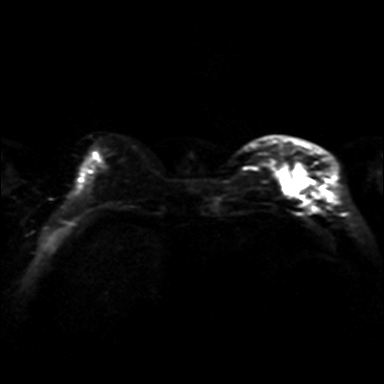
Breast MRI, one axial slice. Slice 9 of 36 in the series (ordered by position). Diffusion-weighted series; image 2 of 4 stored at this slice position (different b-values; order by instance number). 3 T. 384 × 384 image matrix, field of view 320 × 320 mm. Female patient.
Annotated regions visible in this slice (manually delineated by an expert):
- tumour on diffusion-weighted imaging: bounding box <282,166,305,193> (left, top, right, bottom; pixels)